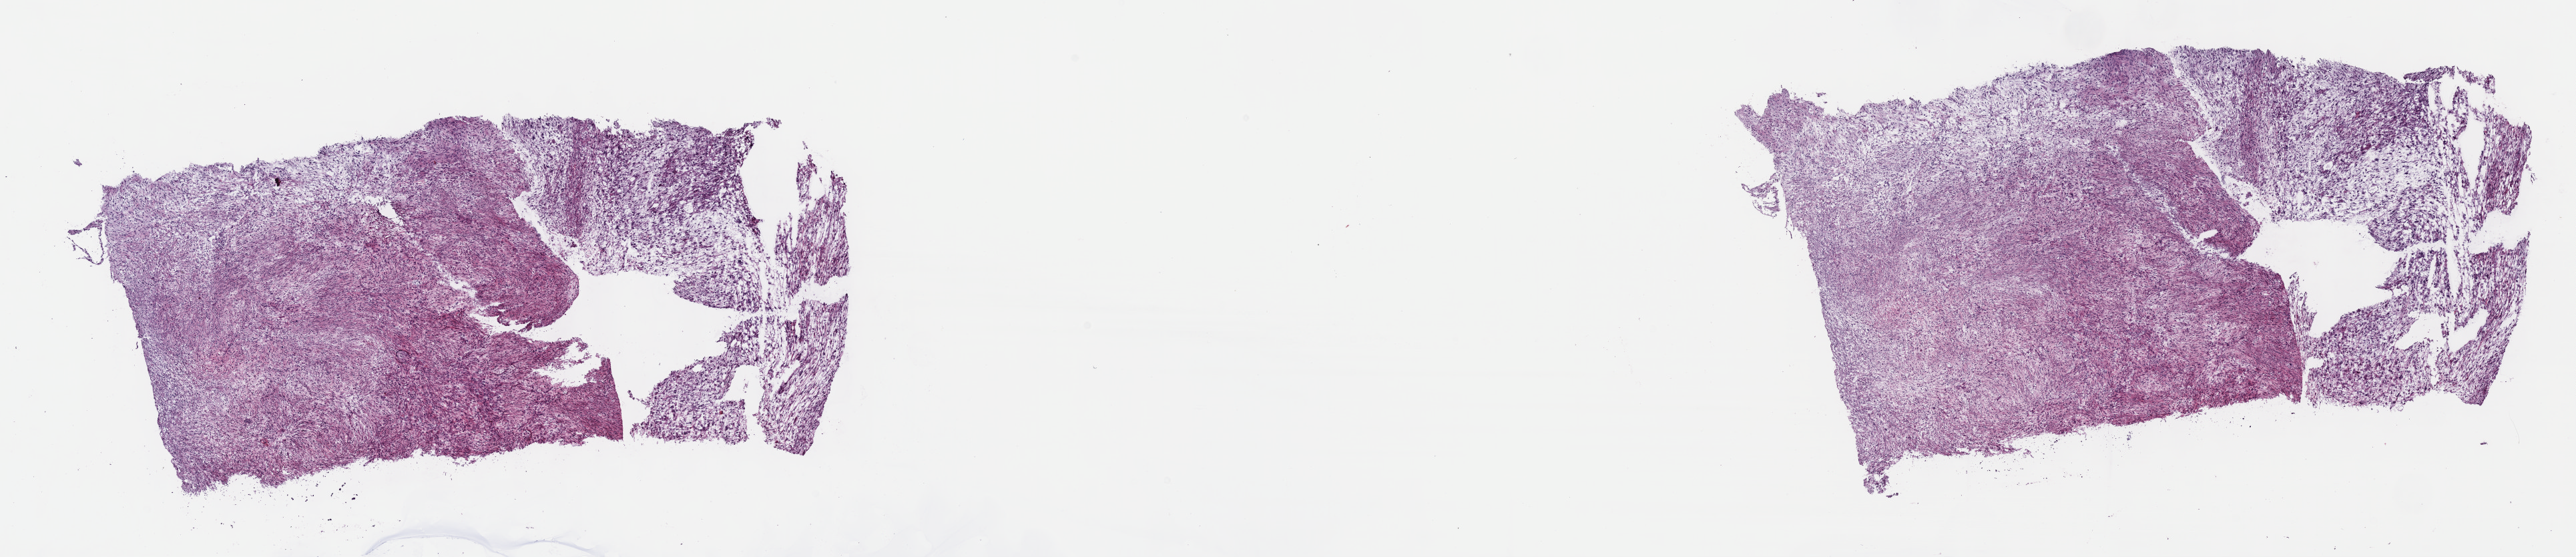
H&E whole-slide image — shown as a low-resolution overview of the whole scanned area (about 31.2 x 6.7 mm, slide scanned at 40x), frozen section from the top of the tissue portion, connective, subcutaneous and other soft tissues, primary tumour sample. Patient sex: male. Pathologist review of this section (percent, as recorded): tumour cells 100%, tumour nuclei 80%, normal cells 0%, stromal cells 0%, necrosis 0%. Infiltration values recorded for this section: lymphocyte infiltration 1%, monocyte infiltration 0%, neutrophil infiltration 0%.
- pathologic diagnosis: Fibromyxosarcoma